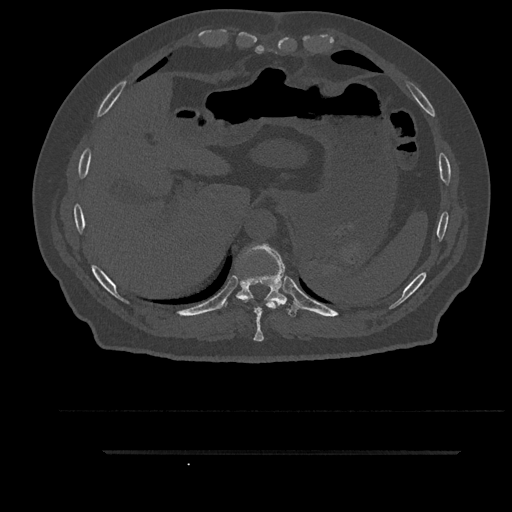
CT including the spine, one axial slice. Slice 391 of 797 in the series (ordered by position). Reconstruction kernel Br40s/3. 120 kVp. Bone window (W 1800 / L 400 HU). 512 × 512 image matrix, field of view 432 × 432 mm. Patient: male, 63 years. From the clinical record (not read from this slice): primary cancer: renal; vertebrae with lytic lesions (as recorded): T8.
Annotated regions visible in this slice (semi-automatically segmented with operator editing):
- T10 vertebra: box from (x=224, y=243) to (x=302, y=317) px
- T9 vertebra: (x=243, y=292)–(x=279, y=342)